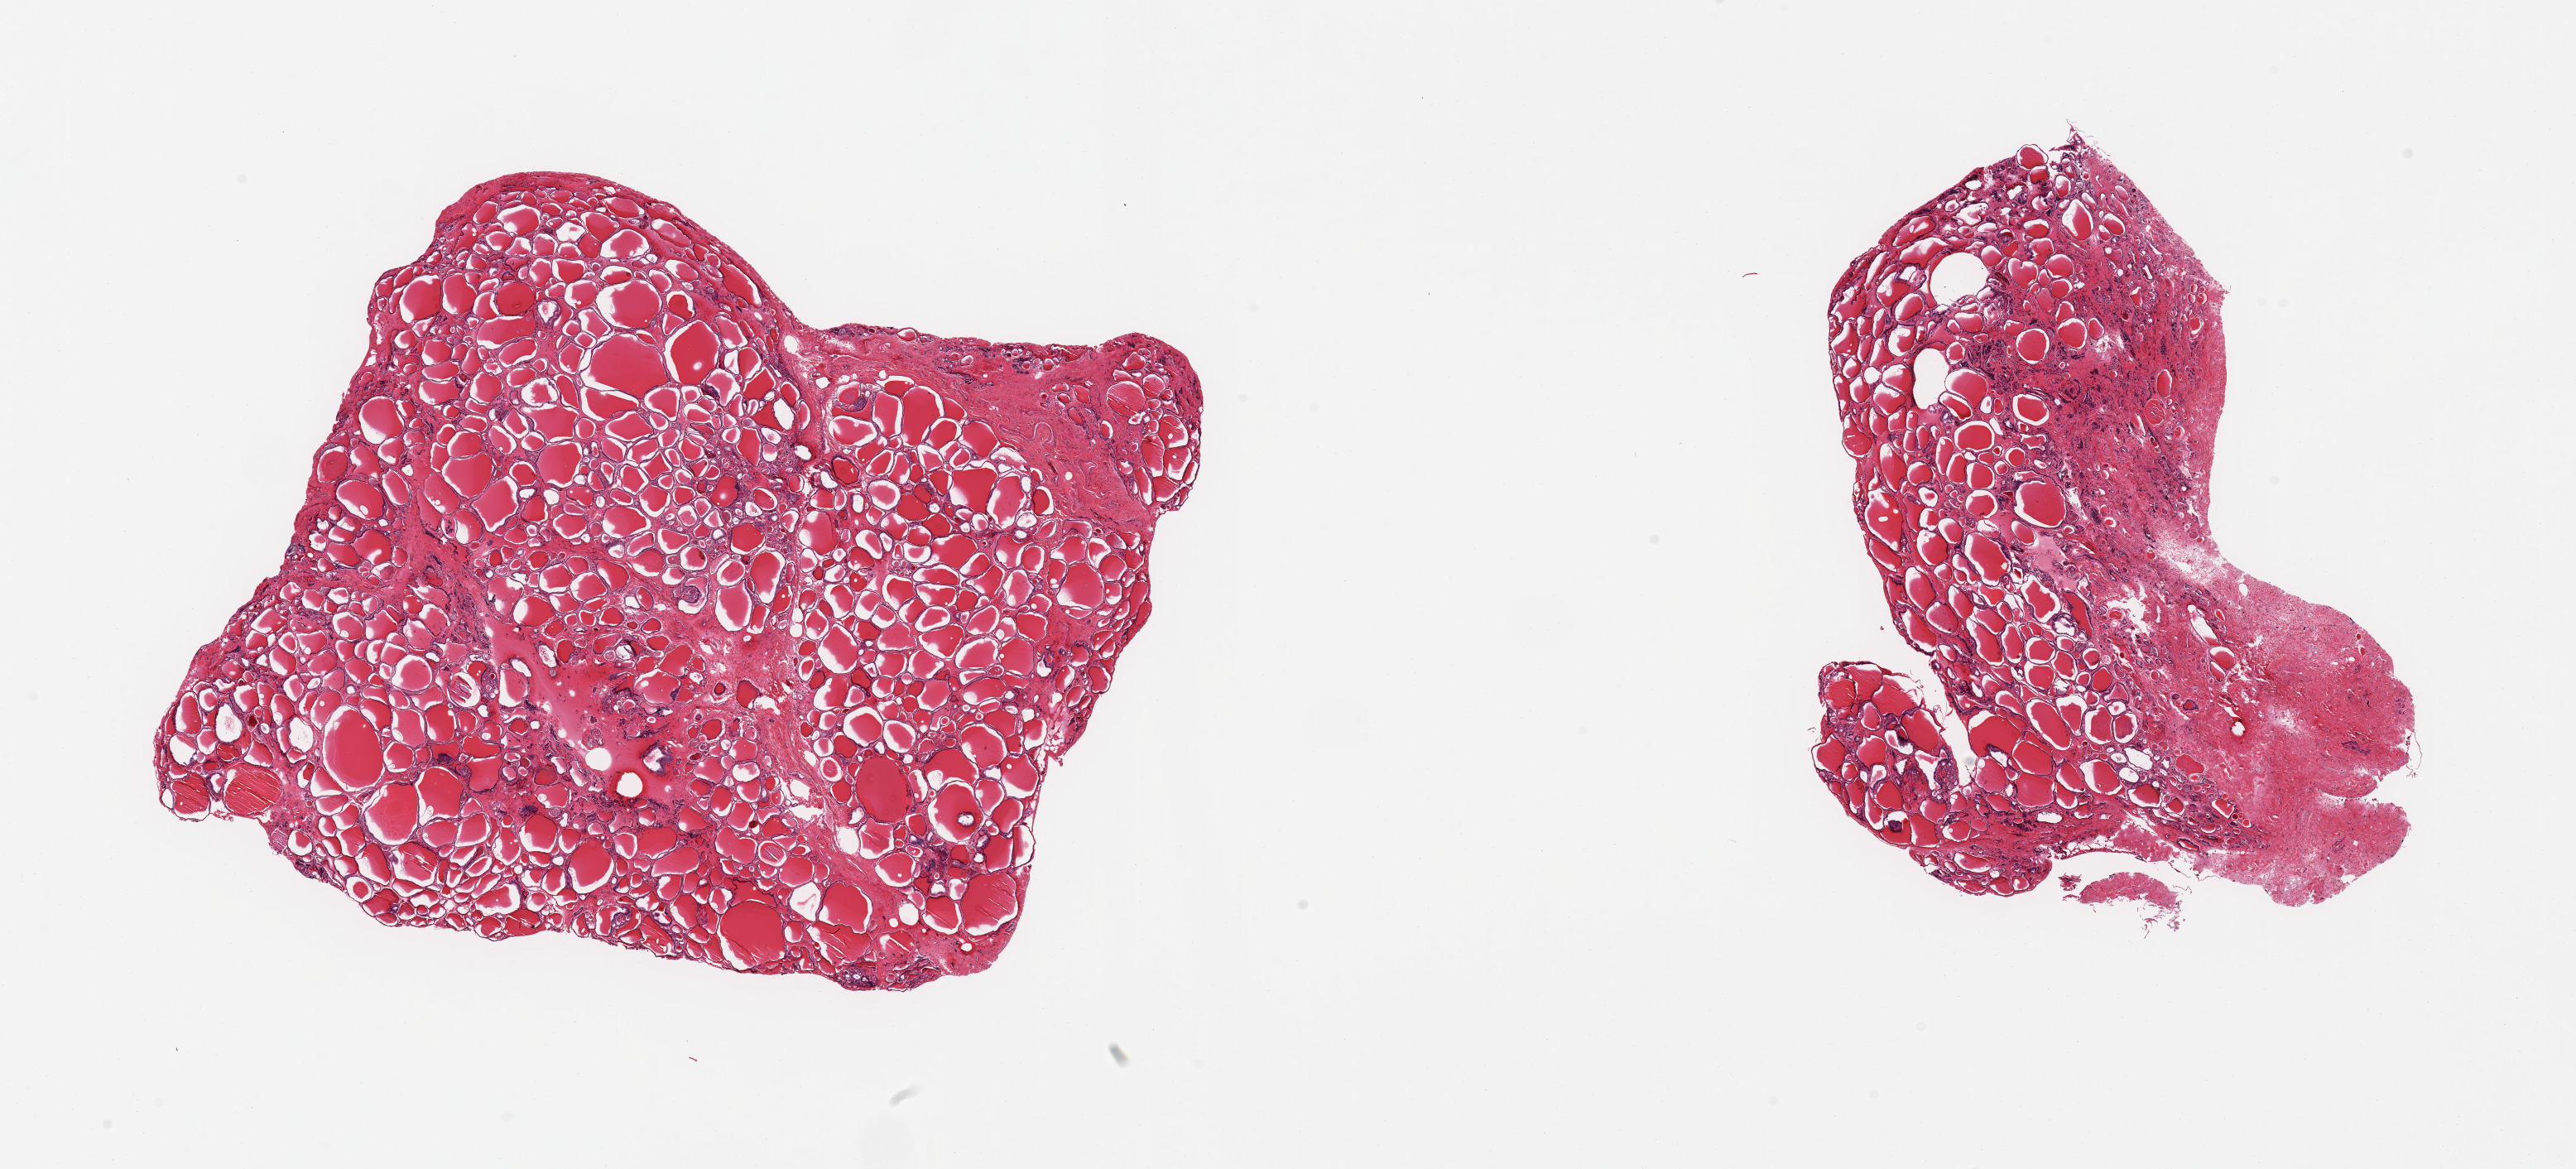
Whole-slide image, haematoxylin and eosin stain, brightfield, low-resolution overview of the scanned area, about 24.6 x 11.2 mm; PAXgene-fixed, paraffin-embedded tissue; sampled site (target tissue): thyroid; tissue donor sample. Female donor.
Reviewer comment on this tissue sample: 2 pieces; smaller piece has 30% fibrous content.